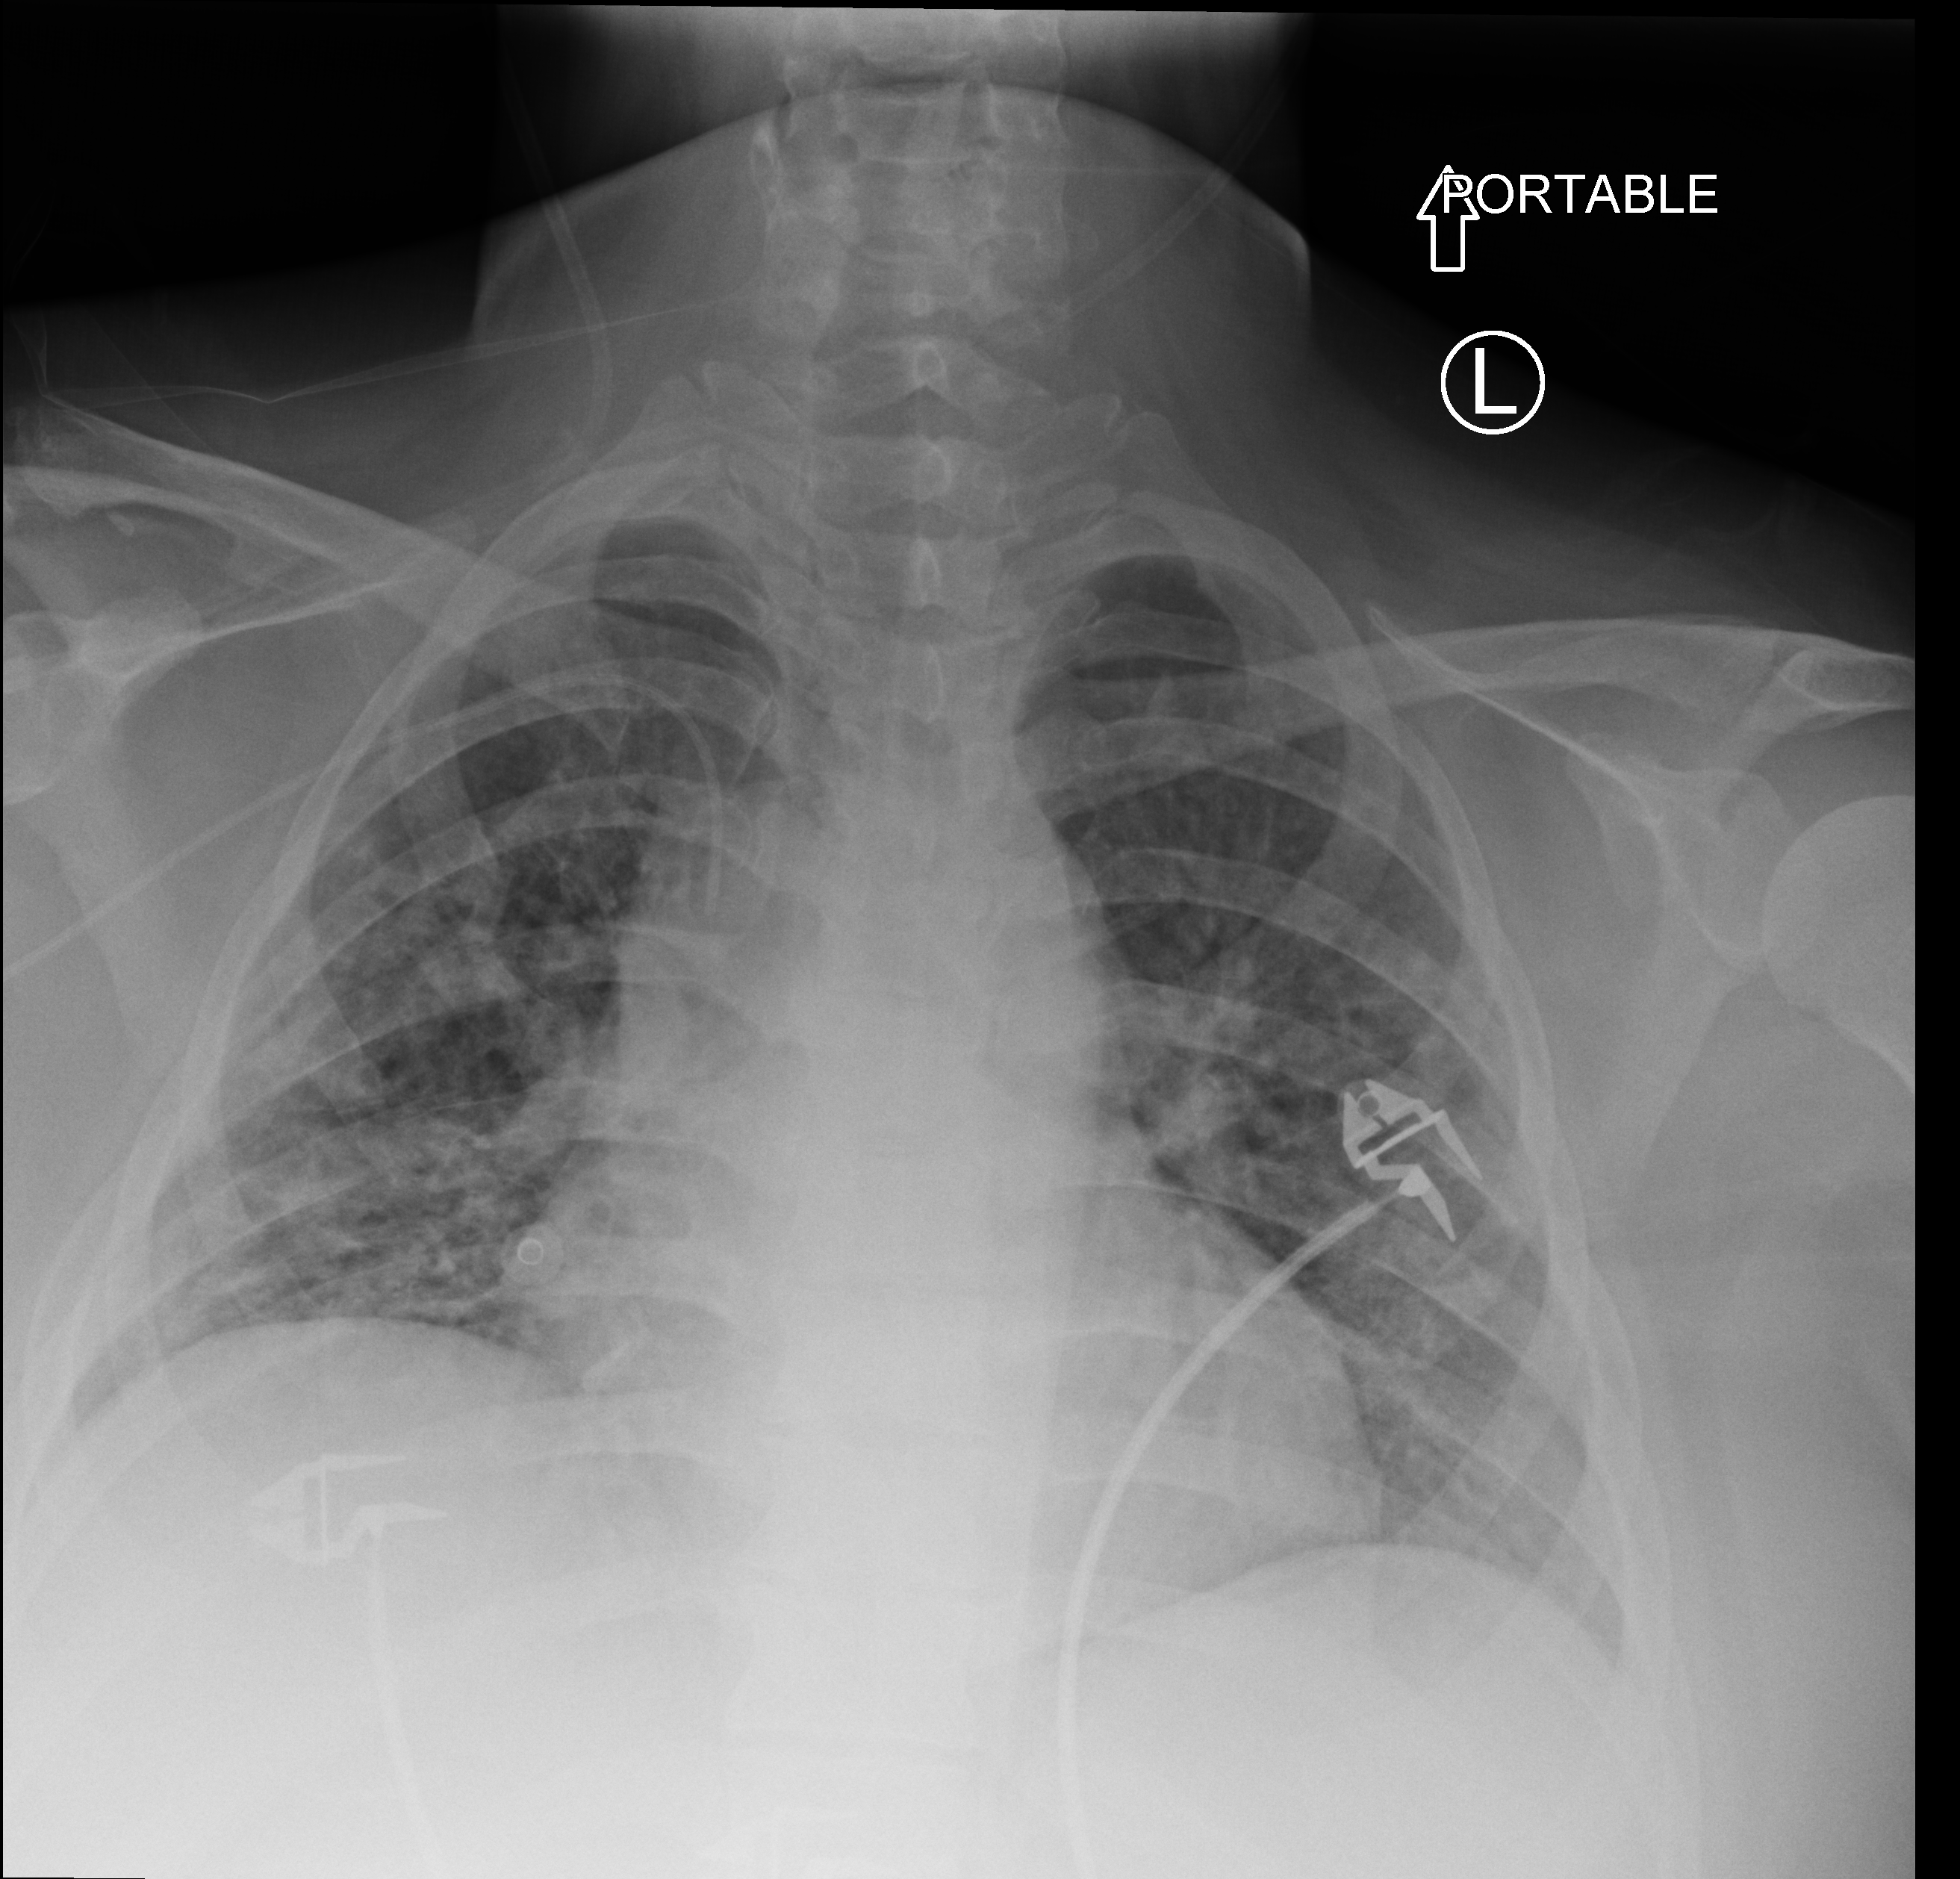
Chest X-ray (portable), anteroposterior (AP) projection. Patient hospitalised with COVID-19; female, aged 18–59 years.
Hospital-stay facts (about this admission, not read from this image; timing relative to this image not recorded):
- admitted to intensive care during this hospital stay: yes